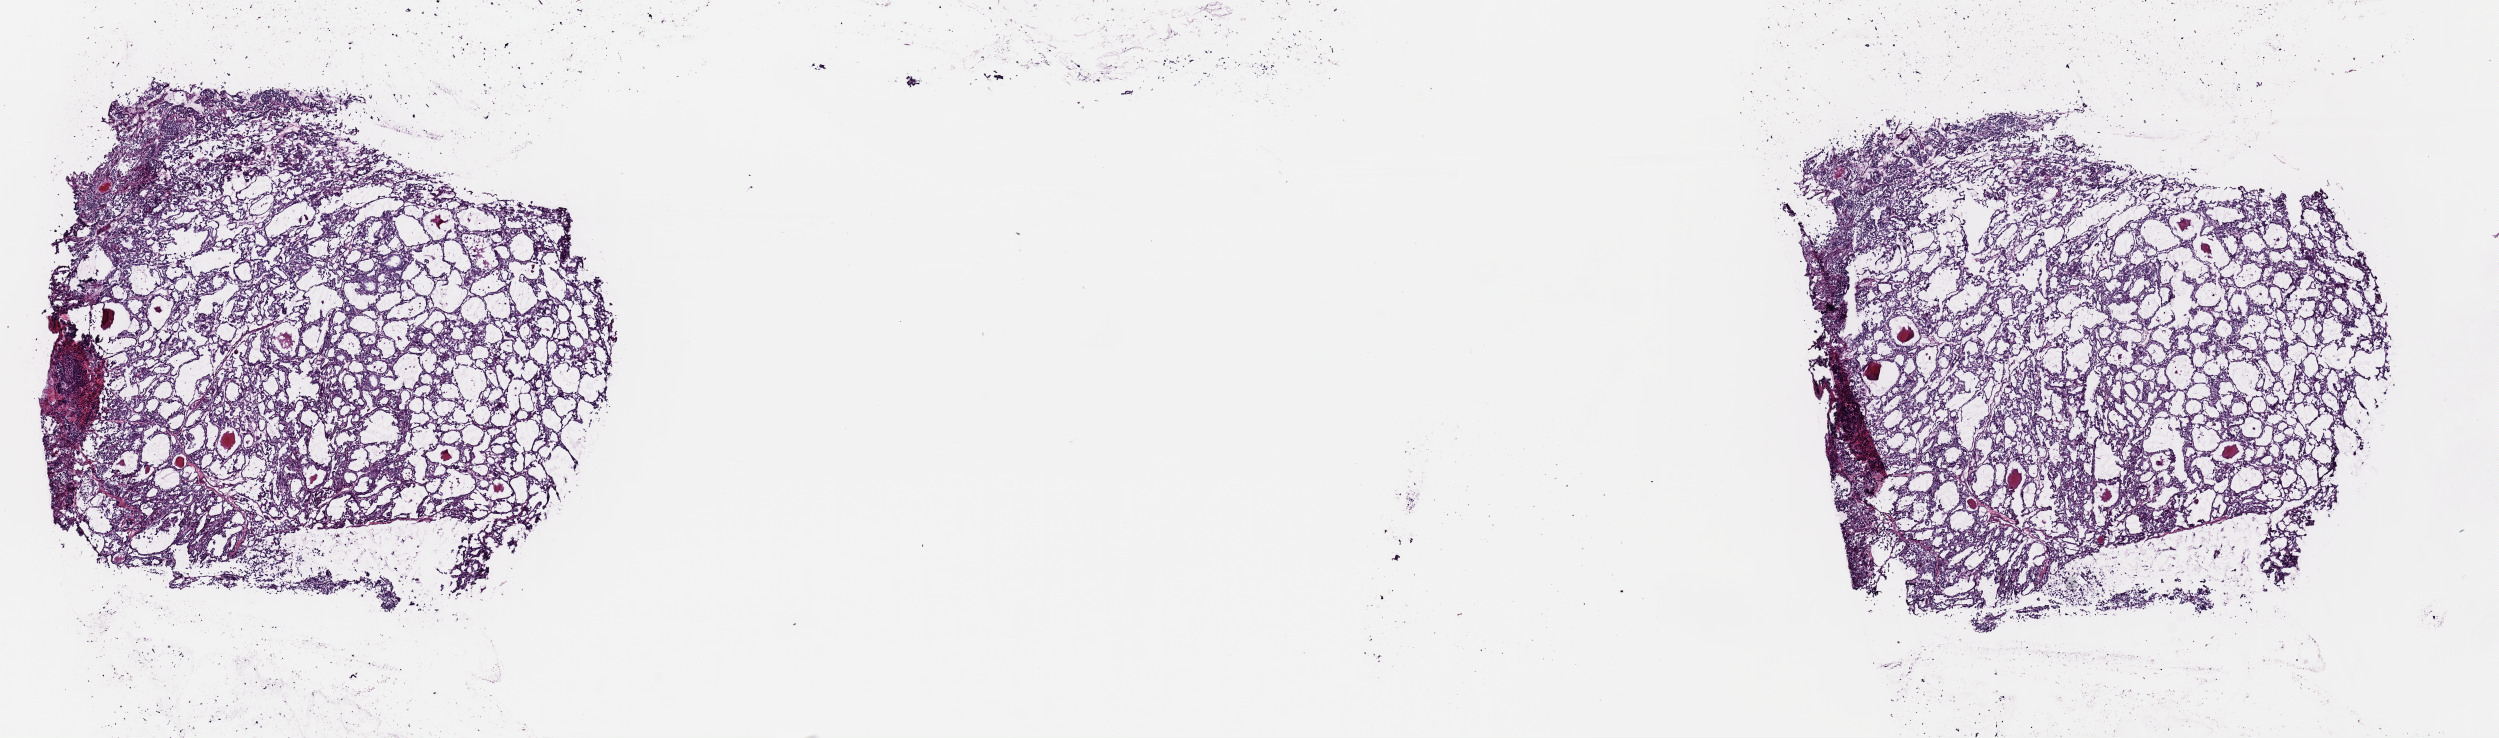
Digitized H&E tissue section (whole slide) — whole scanned area (about 19.7 x 5.8 mm, slide scanned at 40x) shown as a low-resolution overview, frozen section from the top of the tissue portion, thyroid, primary tumour sample. Male patient; age at initial diagnosis 28 years. Pathologist review of this section (percent, as recorded): tumour cells 90%, tumour nuclei 96%, normal cells 0%, stromal cells 10%, necrosis 0%. Infiltration values recorded for this section: lymphocyte infiltration 0%, monocyte infiltration 0%, neutrophil infiltration 0%.
- lymph nodes positive (case pathology): 6 of 25 examined
- diagnosis: Papillary carcinoma, follicular variant (thyroid gland)
- laterality: right
- AJCC pathologic stage: I (7th edition)